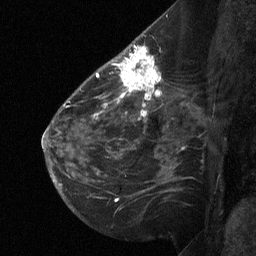
Breast MRI (dynamic contrast-enhanced), one sagittal slice. Slice 38 of 64 in the series (ordered by position). Dynamic contrast-enhanced study with each time point stored as its own series, time point 2 of 3 at this slice position (early post-contrast, ordered by acquisition time). 1.5 T. TE 4.8 ms, TR 27 ms. 2 mm slice thickness. 256 × 256 image matrix, field of view 200 × 200 mm. Female patient, age 51 years. From the clinical record (not read from this slice): setting: breast cancer imaged before/during neoadjuvant chemotherapy; receptor status: HR-positive, HER2-negative.
Outlined on this slice (semi-automatically segmented with operator editing):
- analysis volume of interest (the breast-tissue region the enhancement analysis was run in; not a lesion): bounding box (x1, y1, x2, y2) in pixels: (112, 46, 169, 106)
- tumour enhancement mask (voxels above the 90 % enhancement threshold inside the analysis volume of interest): (118, 46, 161, 106)